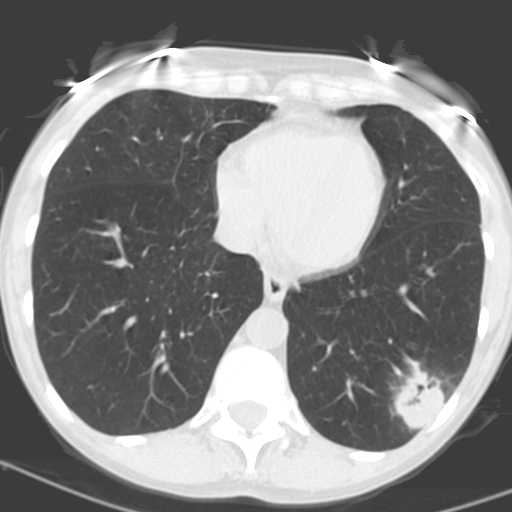
Axial slice from a low-dose chest CT screening exam; baseline annual screen; lung window (W 1500 / L -600 HU); standard (soft-tissue) reconstruction kernel (C); slice 104 of 156 in the series. Female participant, aged 56 years at enrolment. Current smoker at enrolment.
Expert-annotated lung lesion, bounding box (x1, y1, x2, y2) in pixels: (380, 362, 459, 433). The exam's reader record, not a measurement of the box and not confirmed to be the same lesion: non-calcified nodule or mass ≥4 mm, left lower lobe, 31 × 23 mm, poorly defined margins, soft tissue attenuation, pre-existing on the prior screen: no. Participant outcome: lung cancer diagnosed 27 days after this screen — squamous cell carcinoma, NOS, left lower lobe, poorly differentiated (G3), stage IB (AJCC 6th edition), 35 mm at pathology.